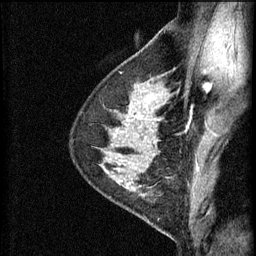
Breast MRI (dynamic contrast-enhanced), one sagittal slice; slice 42 of 60 in the series (ordered by position); 3 images stored at this slice position (order not interpretable as contrast timing); 1.5 T; TE 4.2 ms, TR 11 ms; 256 × 256 image matrix, field of view 180 × 180 mm. Female patient, age 29 years.
Outlined on this slice (semi-automatically segmented with operator editing):
- analysis volume of interest (the breast-tissue region the enhancement analysis was run in; not a lesion): bounding box (x1, y1, x2, y2) in pixels: (105, 172, 171, 227)
- tumour enhancement mask (voxels above the 70 % enhancement threshold inside the analysis volume of interest): (119, 172, 147, 195)